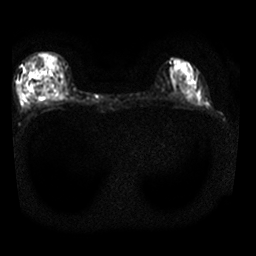
Breast MRI, one axial slice; position 11 of 25 along the scan axis; diffusion-weighted series; image 2 of 4 stored at this slice position (different b-values; order by instance number); 1.5 T; 256 × 256 image matrix. Female patient.
Annotated regions visible in this slice (expert manual segmentation):
- tumour on diffusion-weighted imaging: bounding box <44,88,52,96> (left, top, right, bottom; pixels)